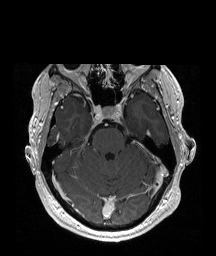
Brain MRI from a brain-tumour surgery series, one axial slice; T1-weighted post-contrast; 1 mm slice thickness; 216 × 256 image matrix, field of view 219 × 260 mm. From the clinical record (not read from this slice): histopathology: Astrocytoma; WHO grade: 2; IDH mutation: yes; tumour location: Right Insular.
Structures marked on this image (expert manual segmentation):
- tumour: bounding box <79,98,82,101> (left, top, right, bottom; pixels)